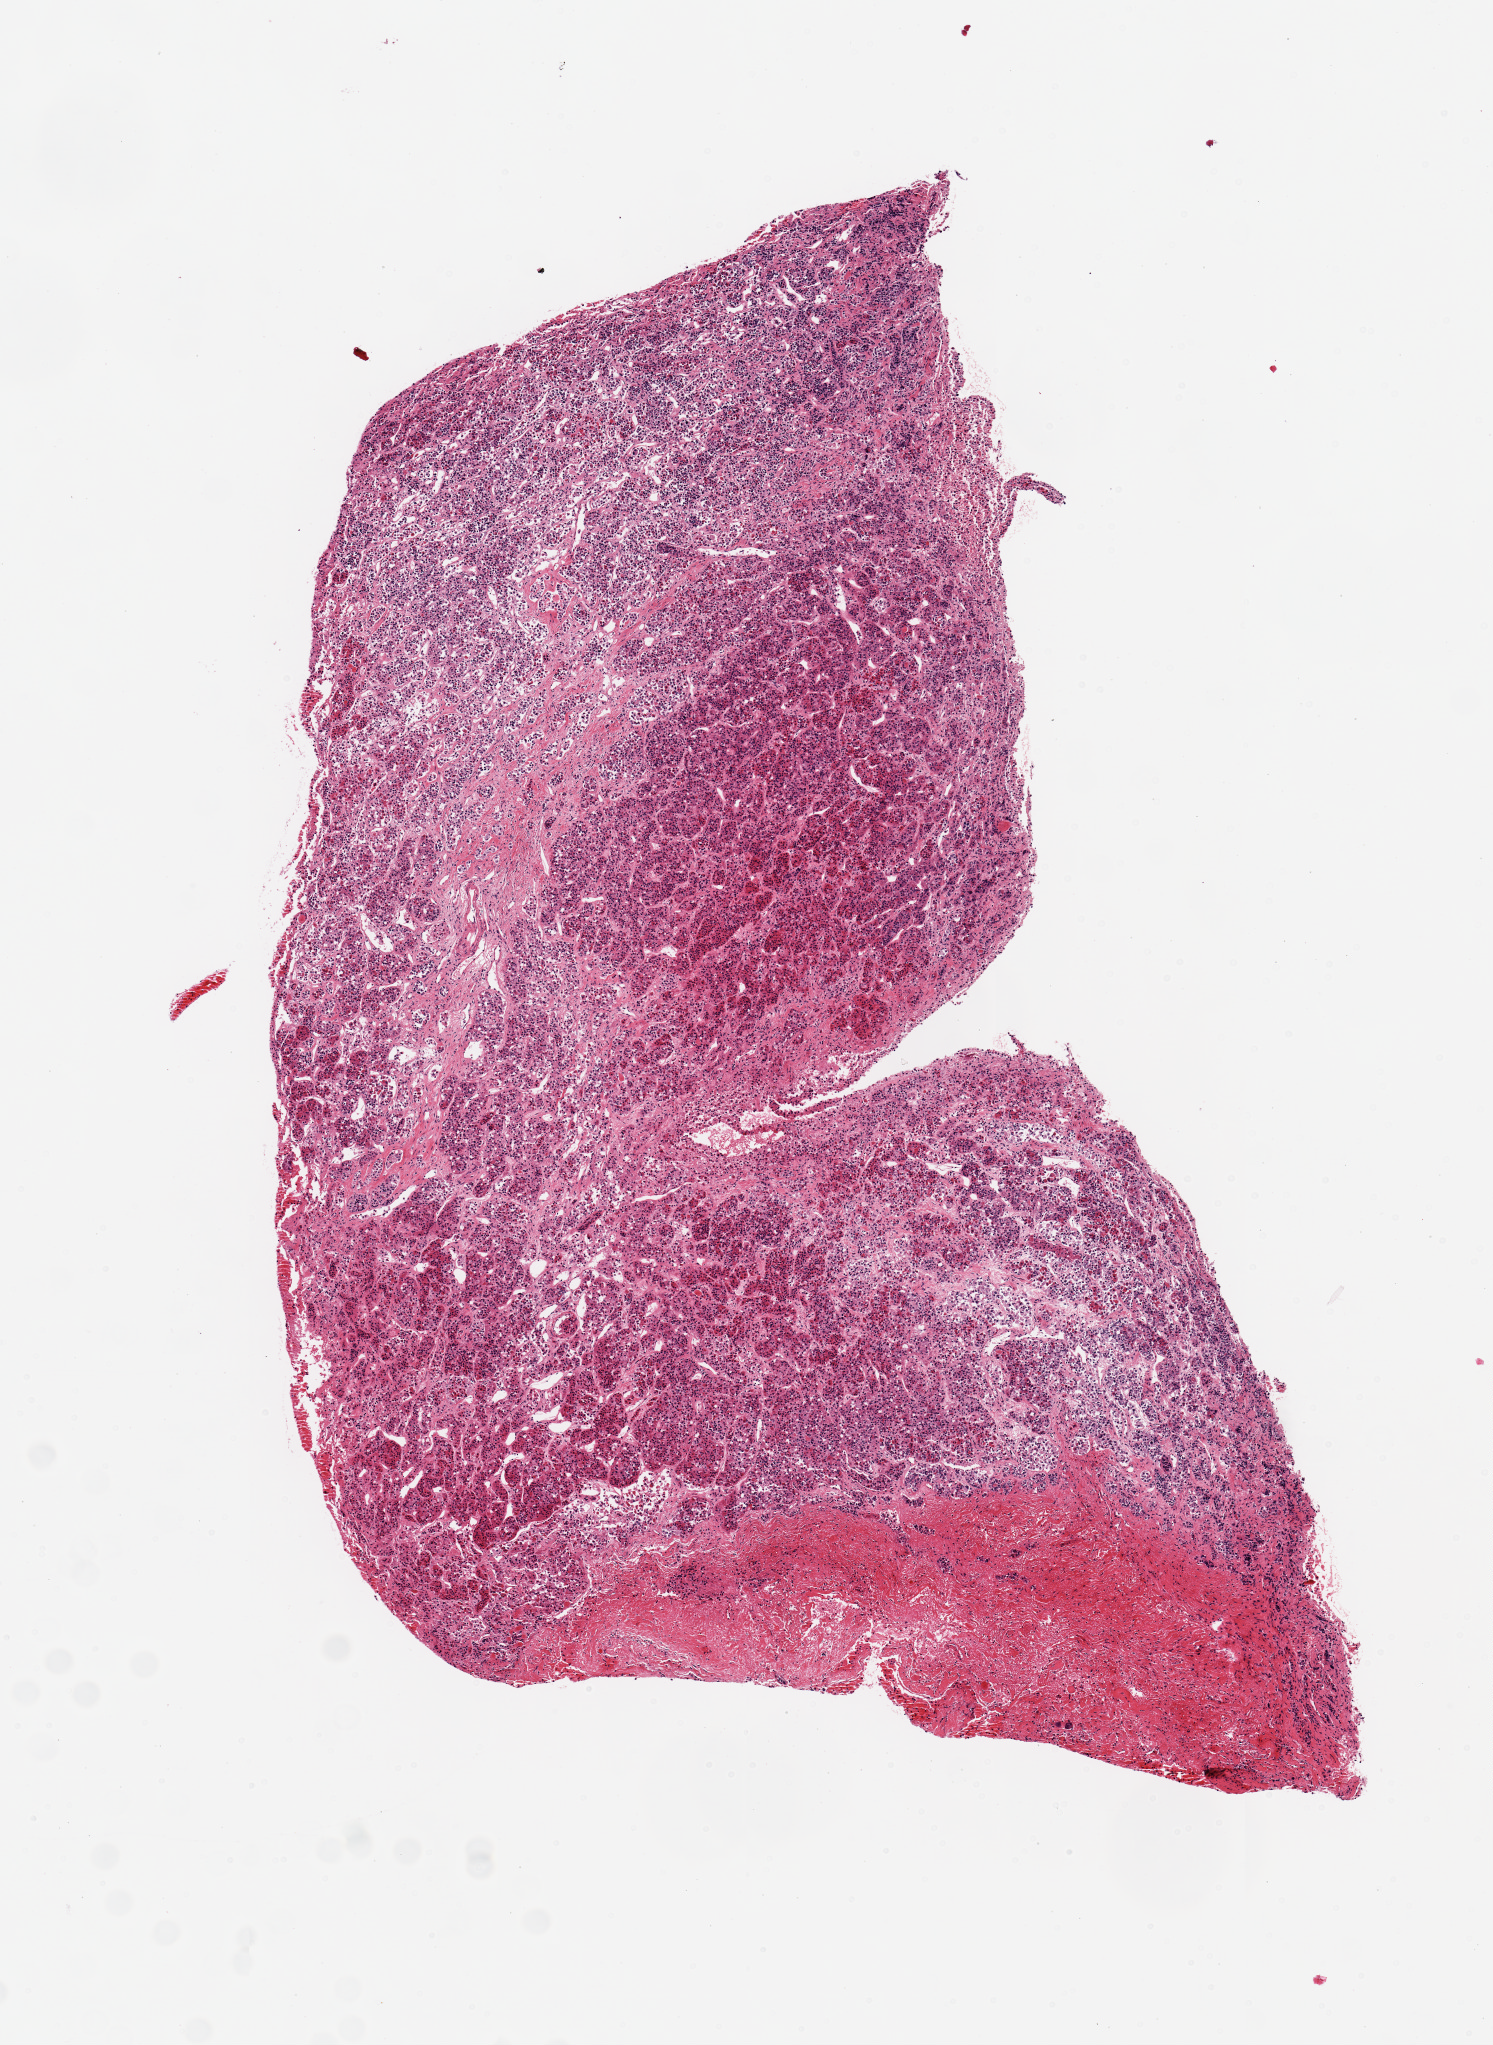
Whole-slide image, hematoxylin and eosin (H&E) stain, a low-resolution overview of the entire scanned area, about 5.9 x 8.1 mm; PAXgene-fixed, paraffin-embedded tissue; sampled site (target tissue): pituitary; tissue donor sample. Donor sex: male.
Reviewer comment on this tissue sample: 1 piece, 7x4mm; 20% hemorrhagic stroma (history of trauma).